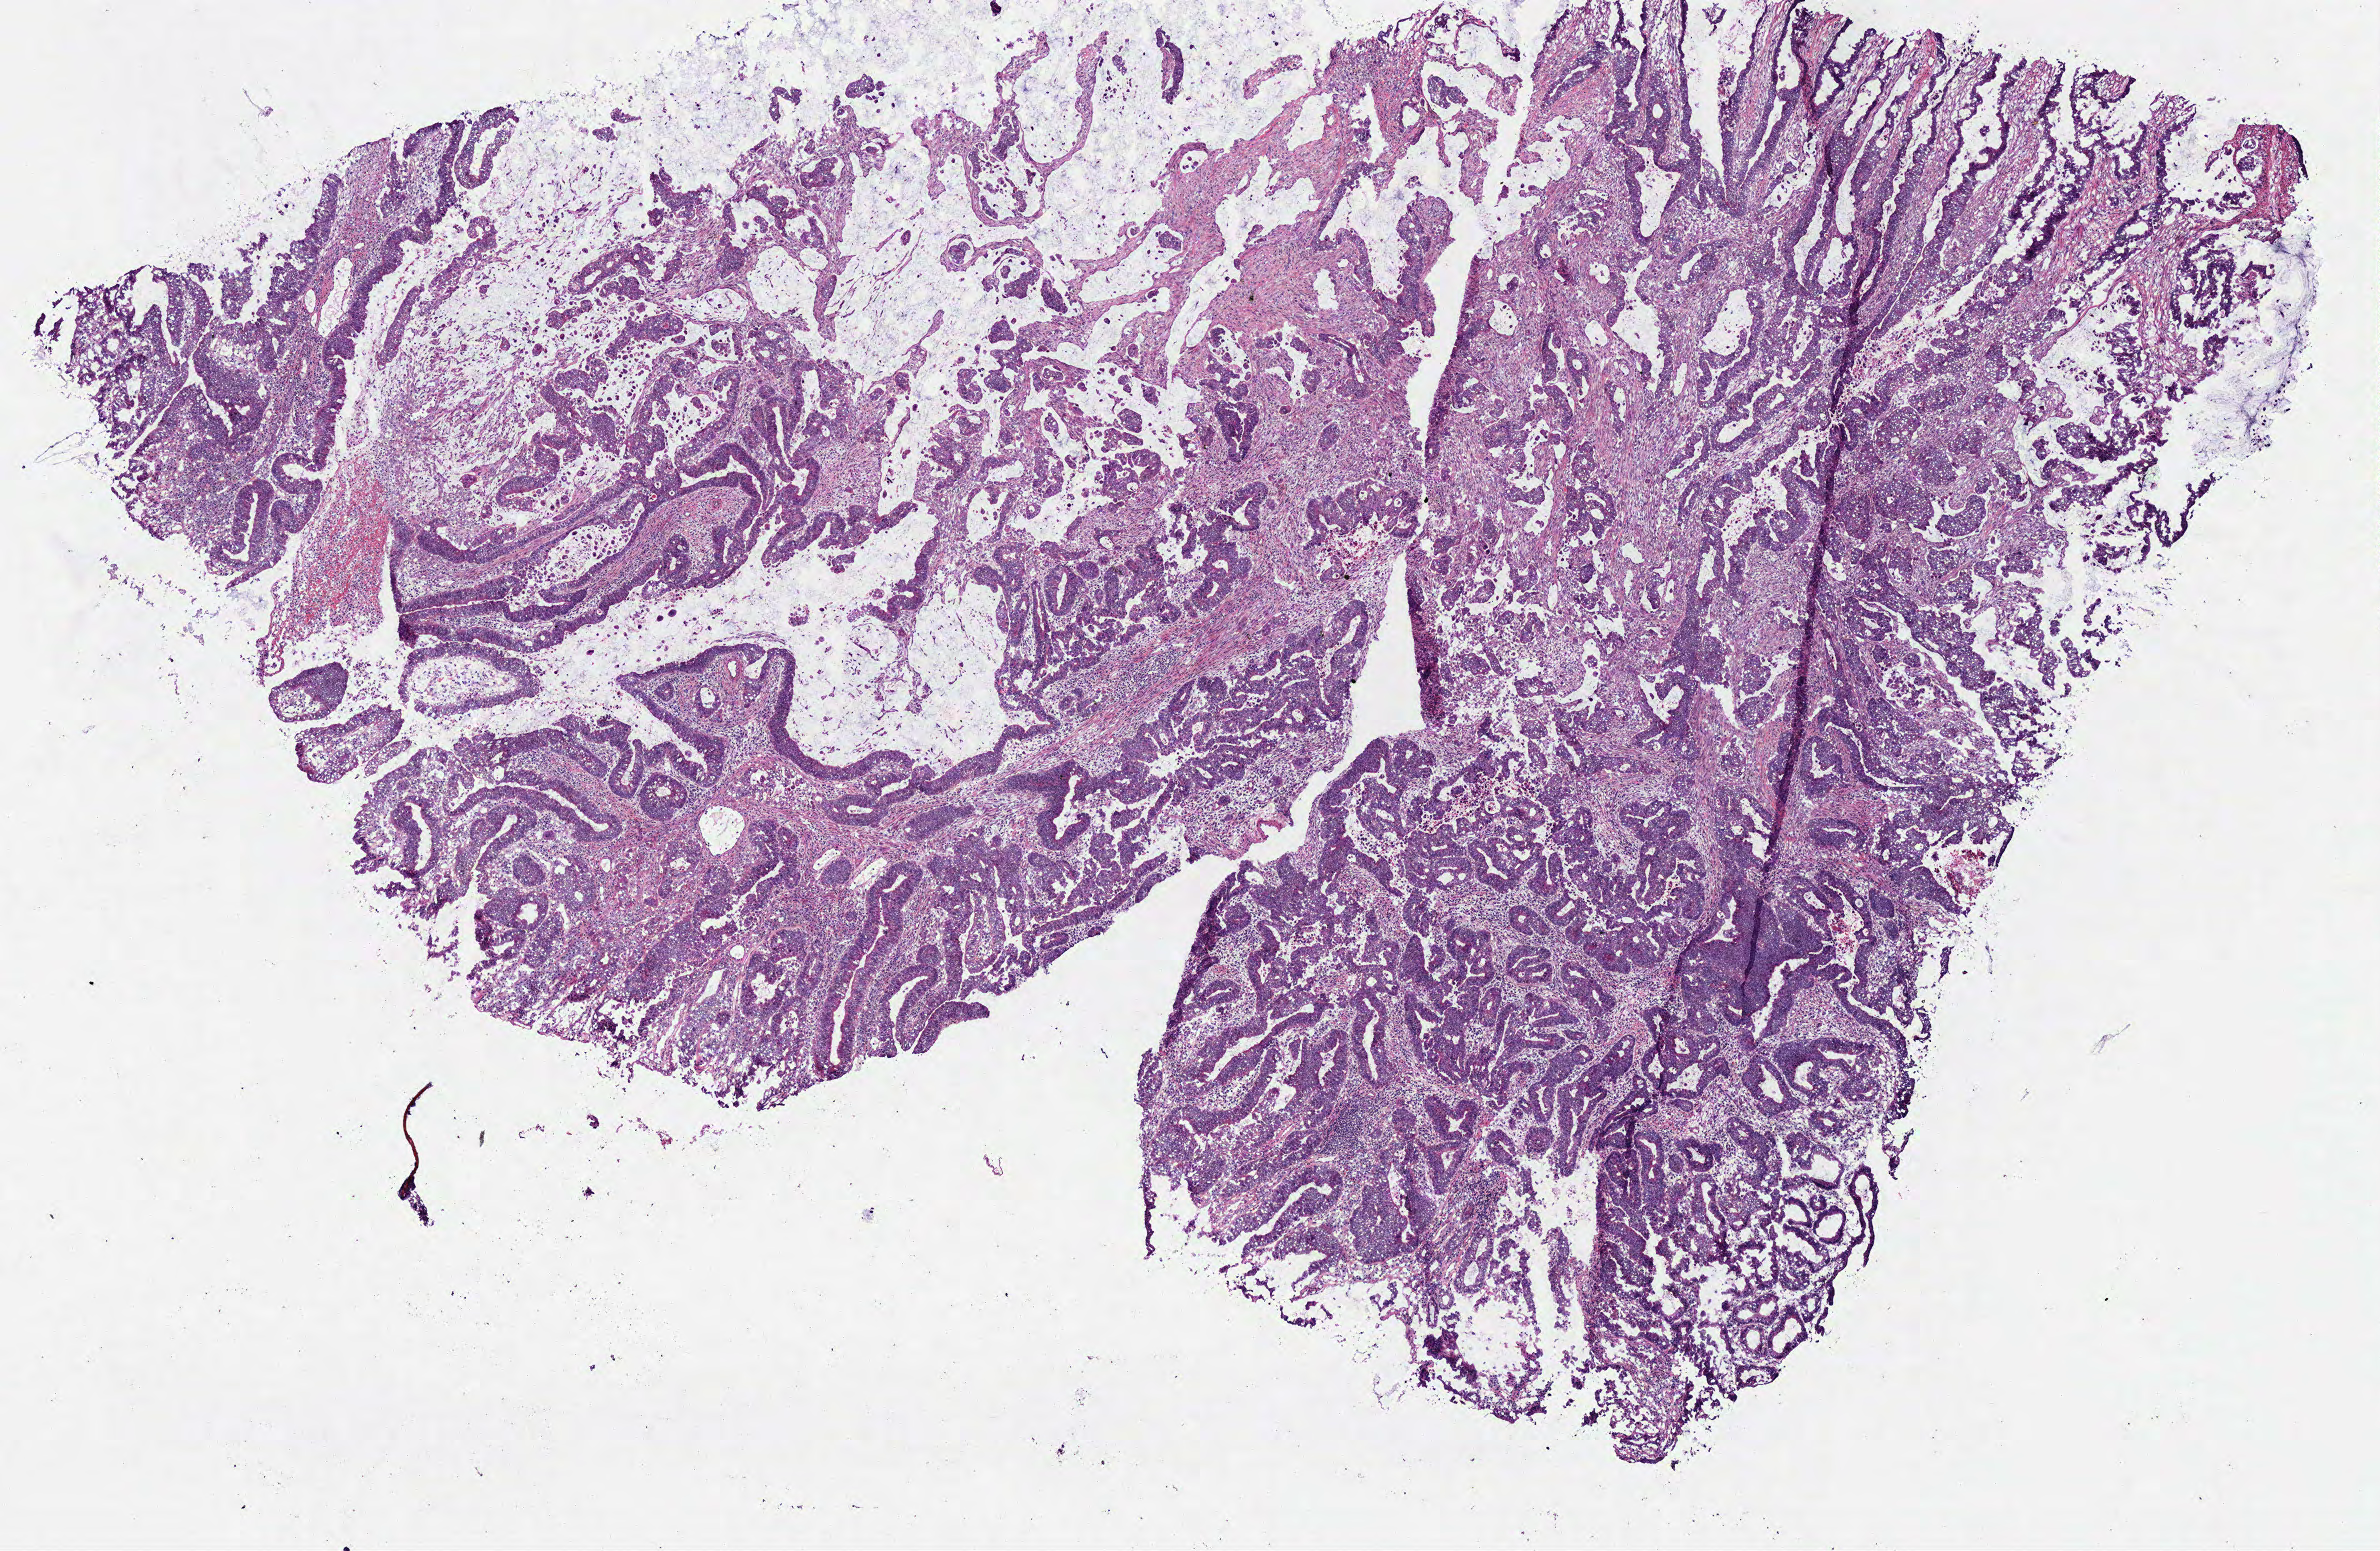
H&E-stained whole-slide image, low-resolution overview of the scanned area, about 9.4 x 6.1 mm. Frozen section. Sample: primary tumour, rectum. Patient: female, age at initial diagnosis 72 years. Slide review estimates, as recorded: tumour cells 98%, tumour nuclei 80%.
Pathologic diagnosis: Adenocarcinoma, NOS (rectosigmoid junction).